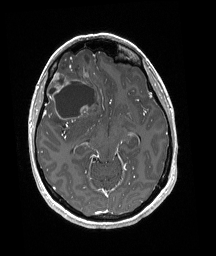
Brain MRI from a brain-tumour surgery series, one axial slice; T1-weighted post-contrast; 1 mm slice thickness; 216 × 256 image matrix, field of view 211 × 250 mm. Case-level facts recorded for this patient, not image findings: histopathology: Oligodendroglioma; WHO grade: 3.
Structures marked on this image (manually delineated by an expert):
- tumour: bounding box <45,52,98,125> (left, top, right, bottom; pixels)